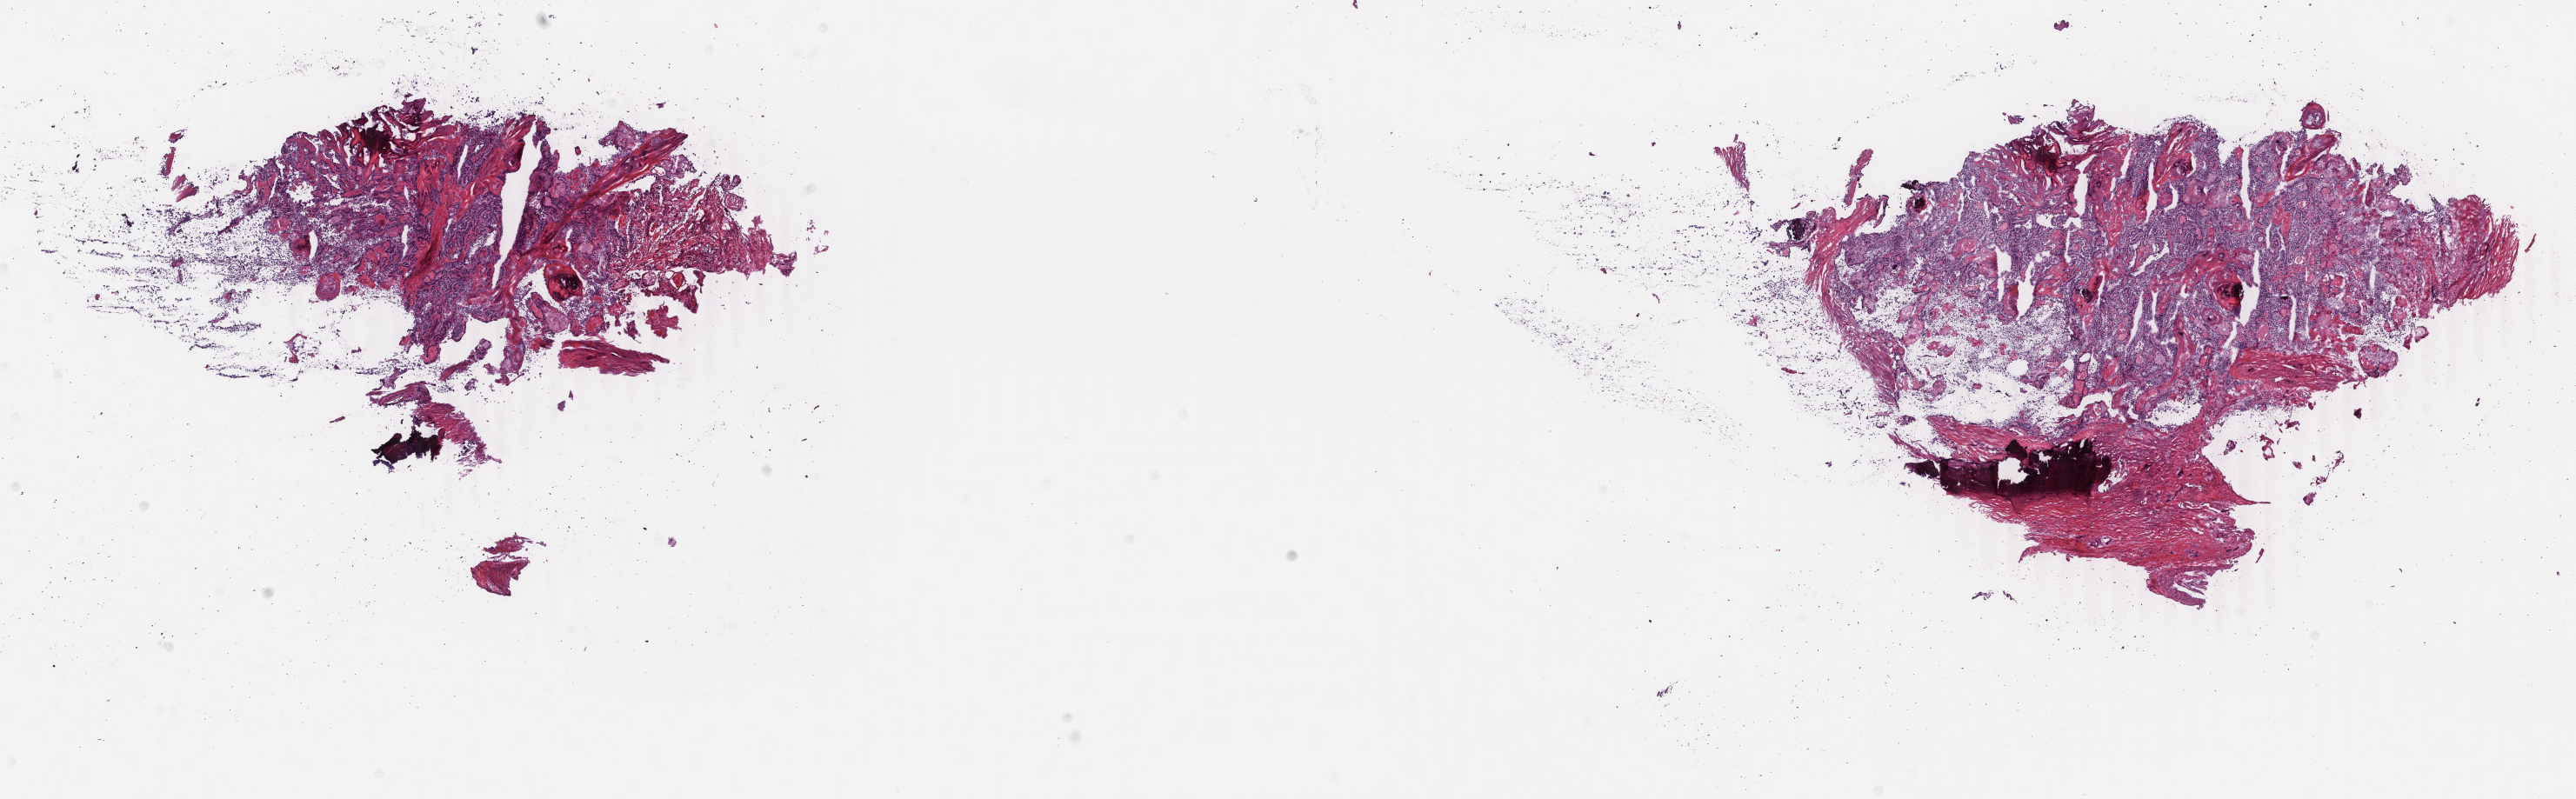
Whole-slide histology image, H&E, shown as a low-resolution overview of the whole scanned area (about 23.6 x 7.3 mm, slide scanned at 40x); frozen section from the top of the tissue portion; thyroid, primary tumour sample. Patient: male, age at initial diagnosis 56 years. Pathologist review of this section (percent, as recorded): tumour cells 80%, tumour nuclei 90%, normal cells 0%, stromal cells 20%, necrosis 0%. Inflammatory infiltration, as recorded: lymphocyte infiltration 0%, monocyte infiltration 0%, neutrophil infiltration 0%.
AJCC pathologic stage: I. Histologic diagnosis: Papillary adenocarcinoma, NOS (thyroid gland). Lymph nodes positive (case pathology): 0 of 6 examined. Laterality: right.